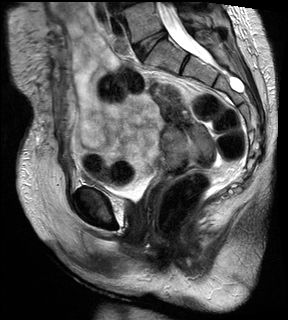
Pelvic MRI for cervical cancer, one sagittal slice. Slice 14 of 28 in the series (ordered by position). T2-weighted. 1.5 T. TE 89 ms, TR 2740 ms. 288 × 320 image matrix, field of view 234 × 260 mm. Patient: female, 59 years.
Annotated regions visible in this slice (expert manual segmentation):
- uterus and cervix: box from (x=149, y=82) to (x=217, y=173) px